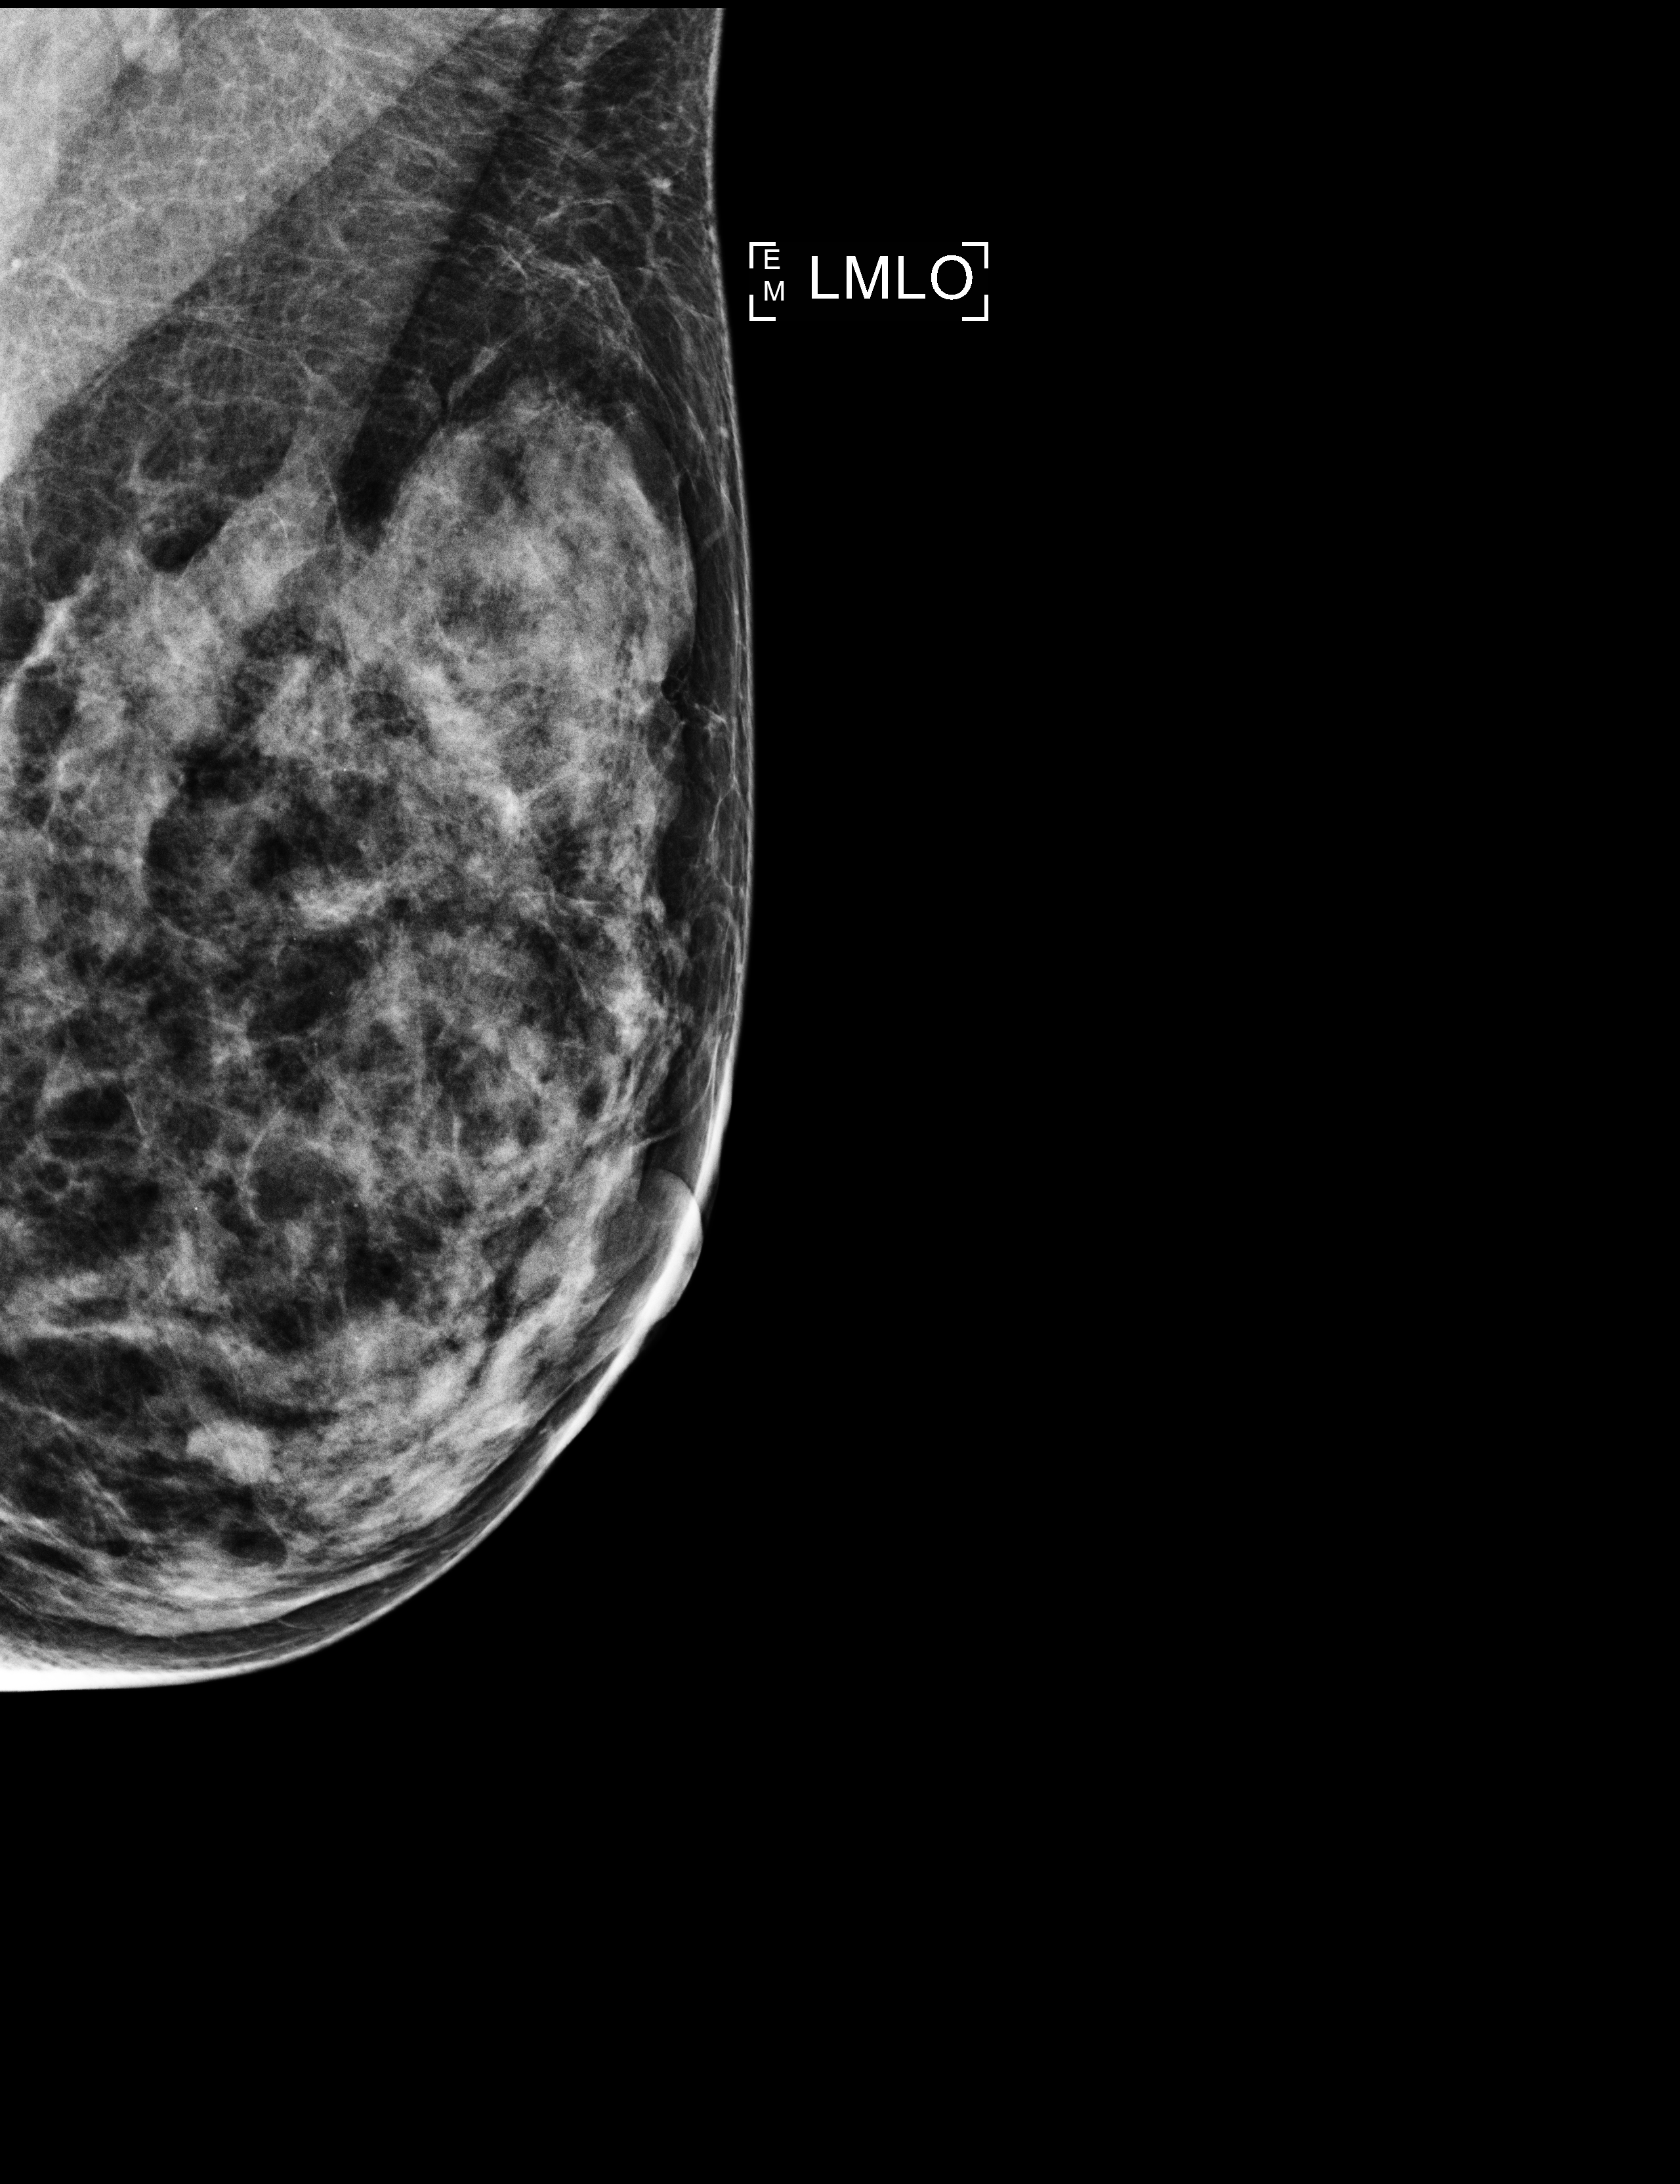
Screening examination. Patient aged 46 years (female).
Image type: full-field digital mammogram. Breast: left. Projection: mediolateral oblique (MLO) view.